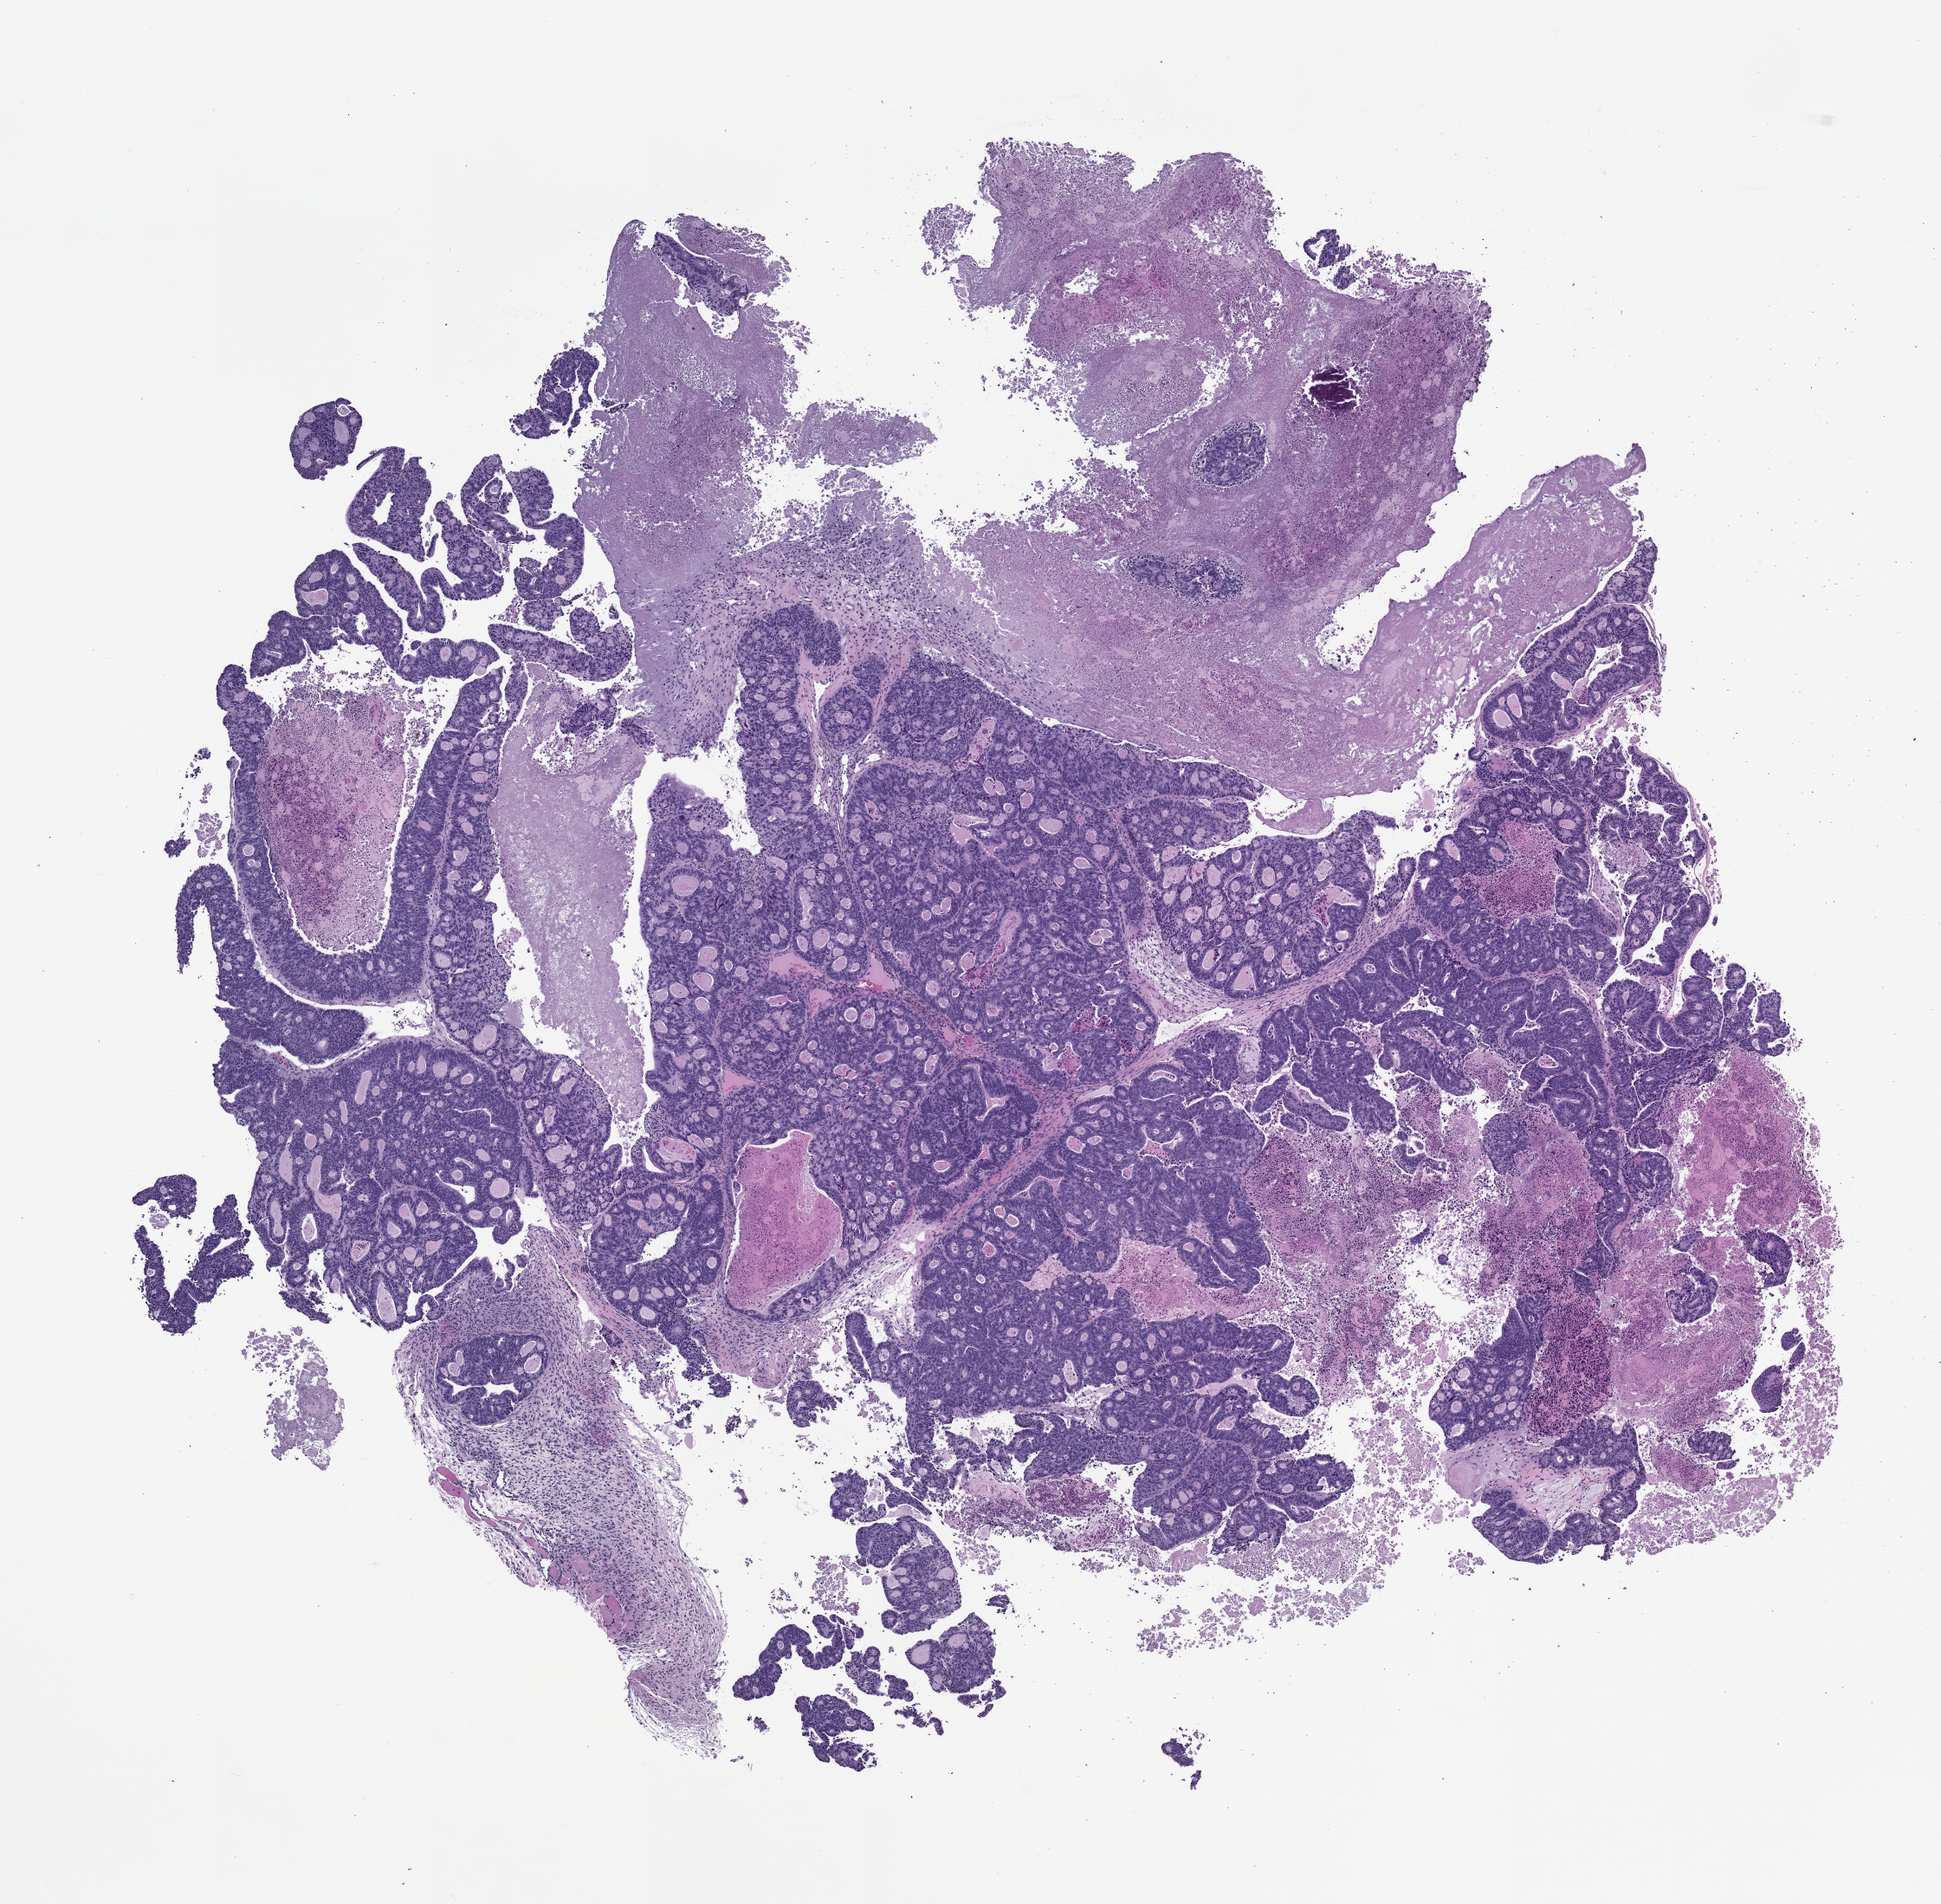
Whole-slide image, haematoxylin and eosin: patient-derived xenograft (human tumor grown in a mouse), passage 0 — low-resolution overview of the scanned area, about 9.0 x 8.8 mm; FFPE section; tumor site category: colon.
* originating patient diagnosis: Colon Adenocarcinoma